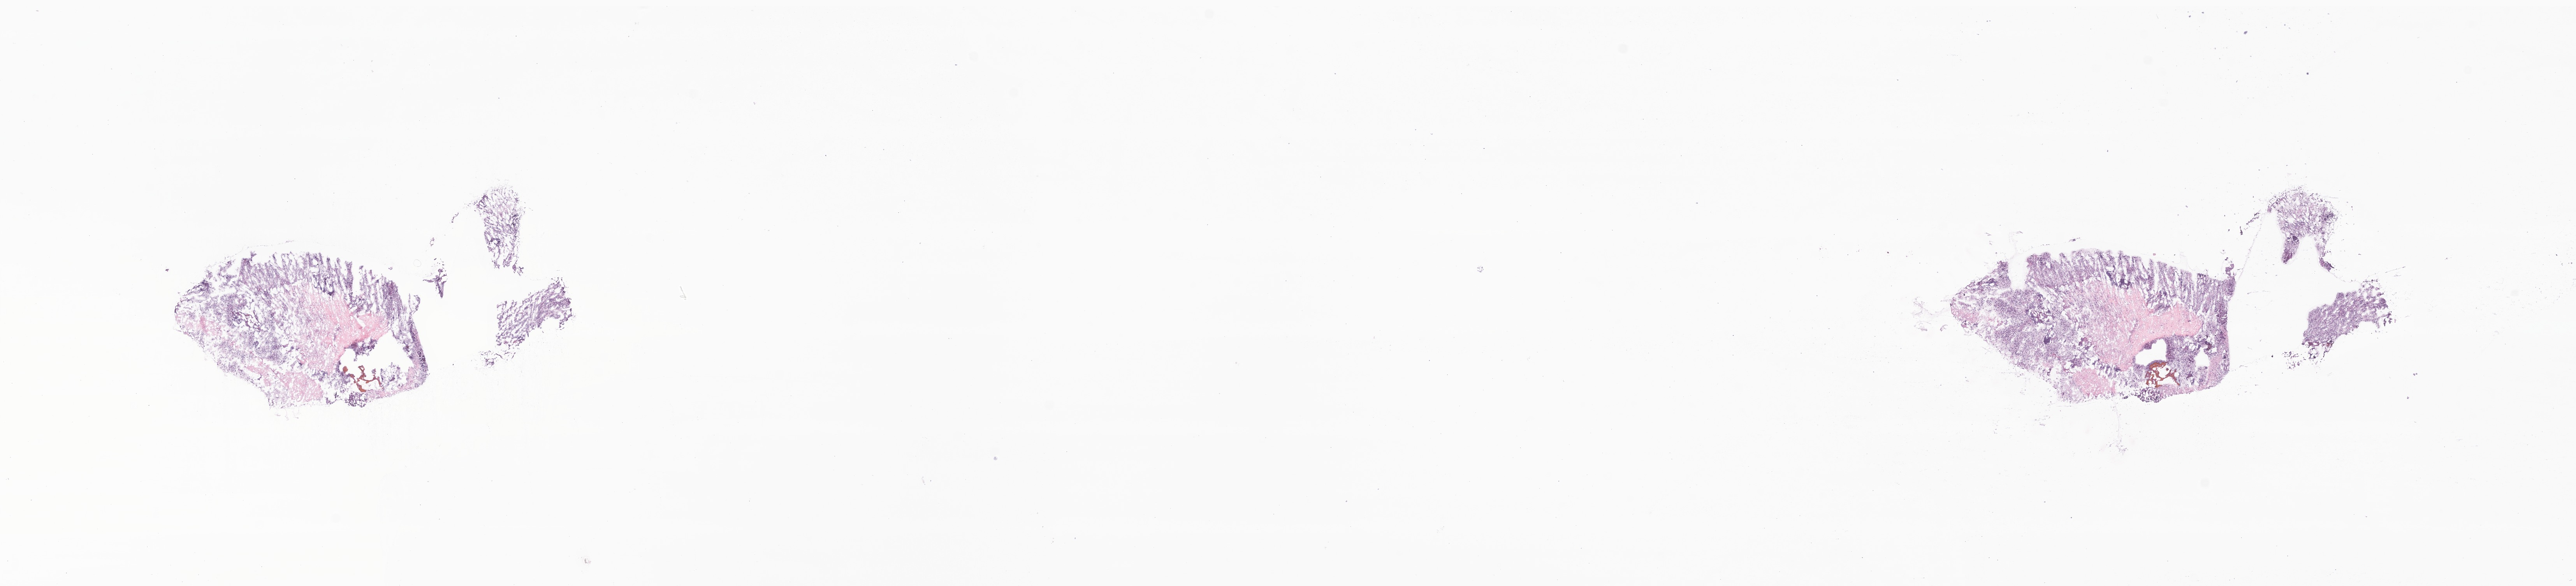
Digitized H&E-stained section of tumor tissue from the brain, a low-resolution overview of the entire scanned area, about 27.9 x 6.3 mm; frozen section (OCT-embedded). Patient male; age 123 months.
Recorded diagnosis: Medulloblastoma, NOS.